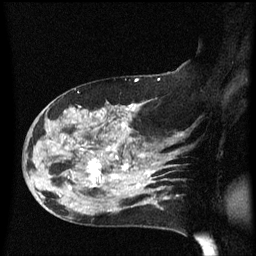
Breast MRI (dynamic contrast-enhanced), one sagittal slice; slice 37 of 60 in the series (ordered by position); dynamic contrast-enhanced series, image 2 of 3 at this slice position (ordered by acquisition); 1.5 T; TE 4.2 ms, TR 8.4 ms; 256 × 256 image matrix, field of view 200 × 200 mm. Patient: female, 47 years.
Outlined on this slice (semi-automatic segmentation, software-assisted and operator-edited):
- analysis volume of interest (the breast-tissue region the enhancement analysis was run in; not a lesion): bounding box <24,97,149,206> (left, top, right, bottom; pixels)
- tumour enhancement mask (voxels above the 70 % enhancement threshold inside the analysis volume of interest): <60,105,149,205>